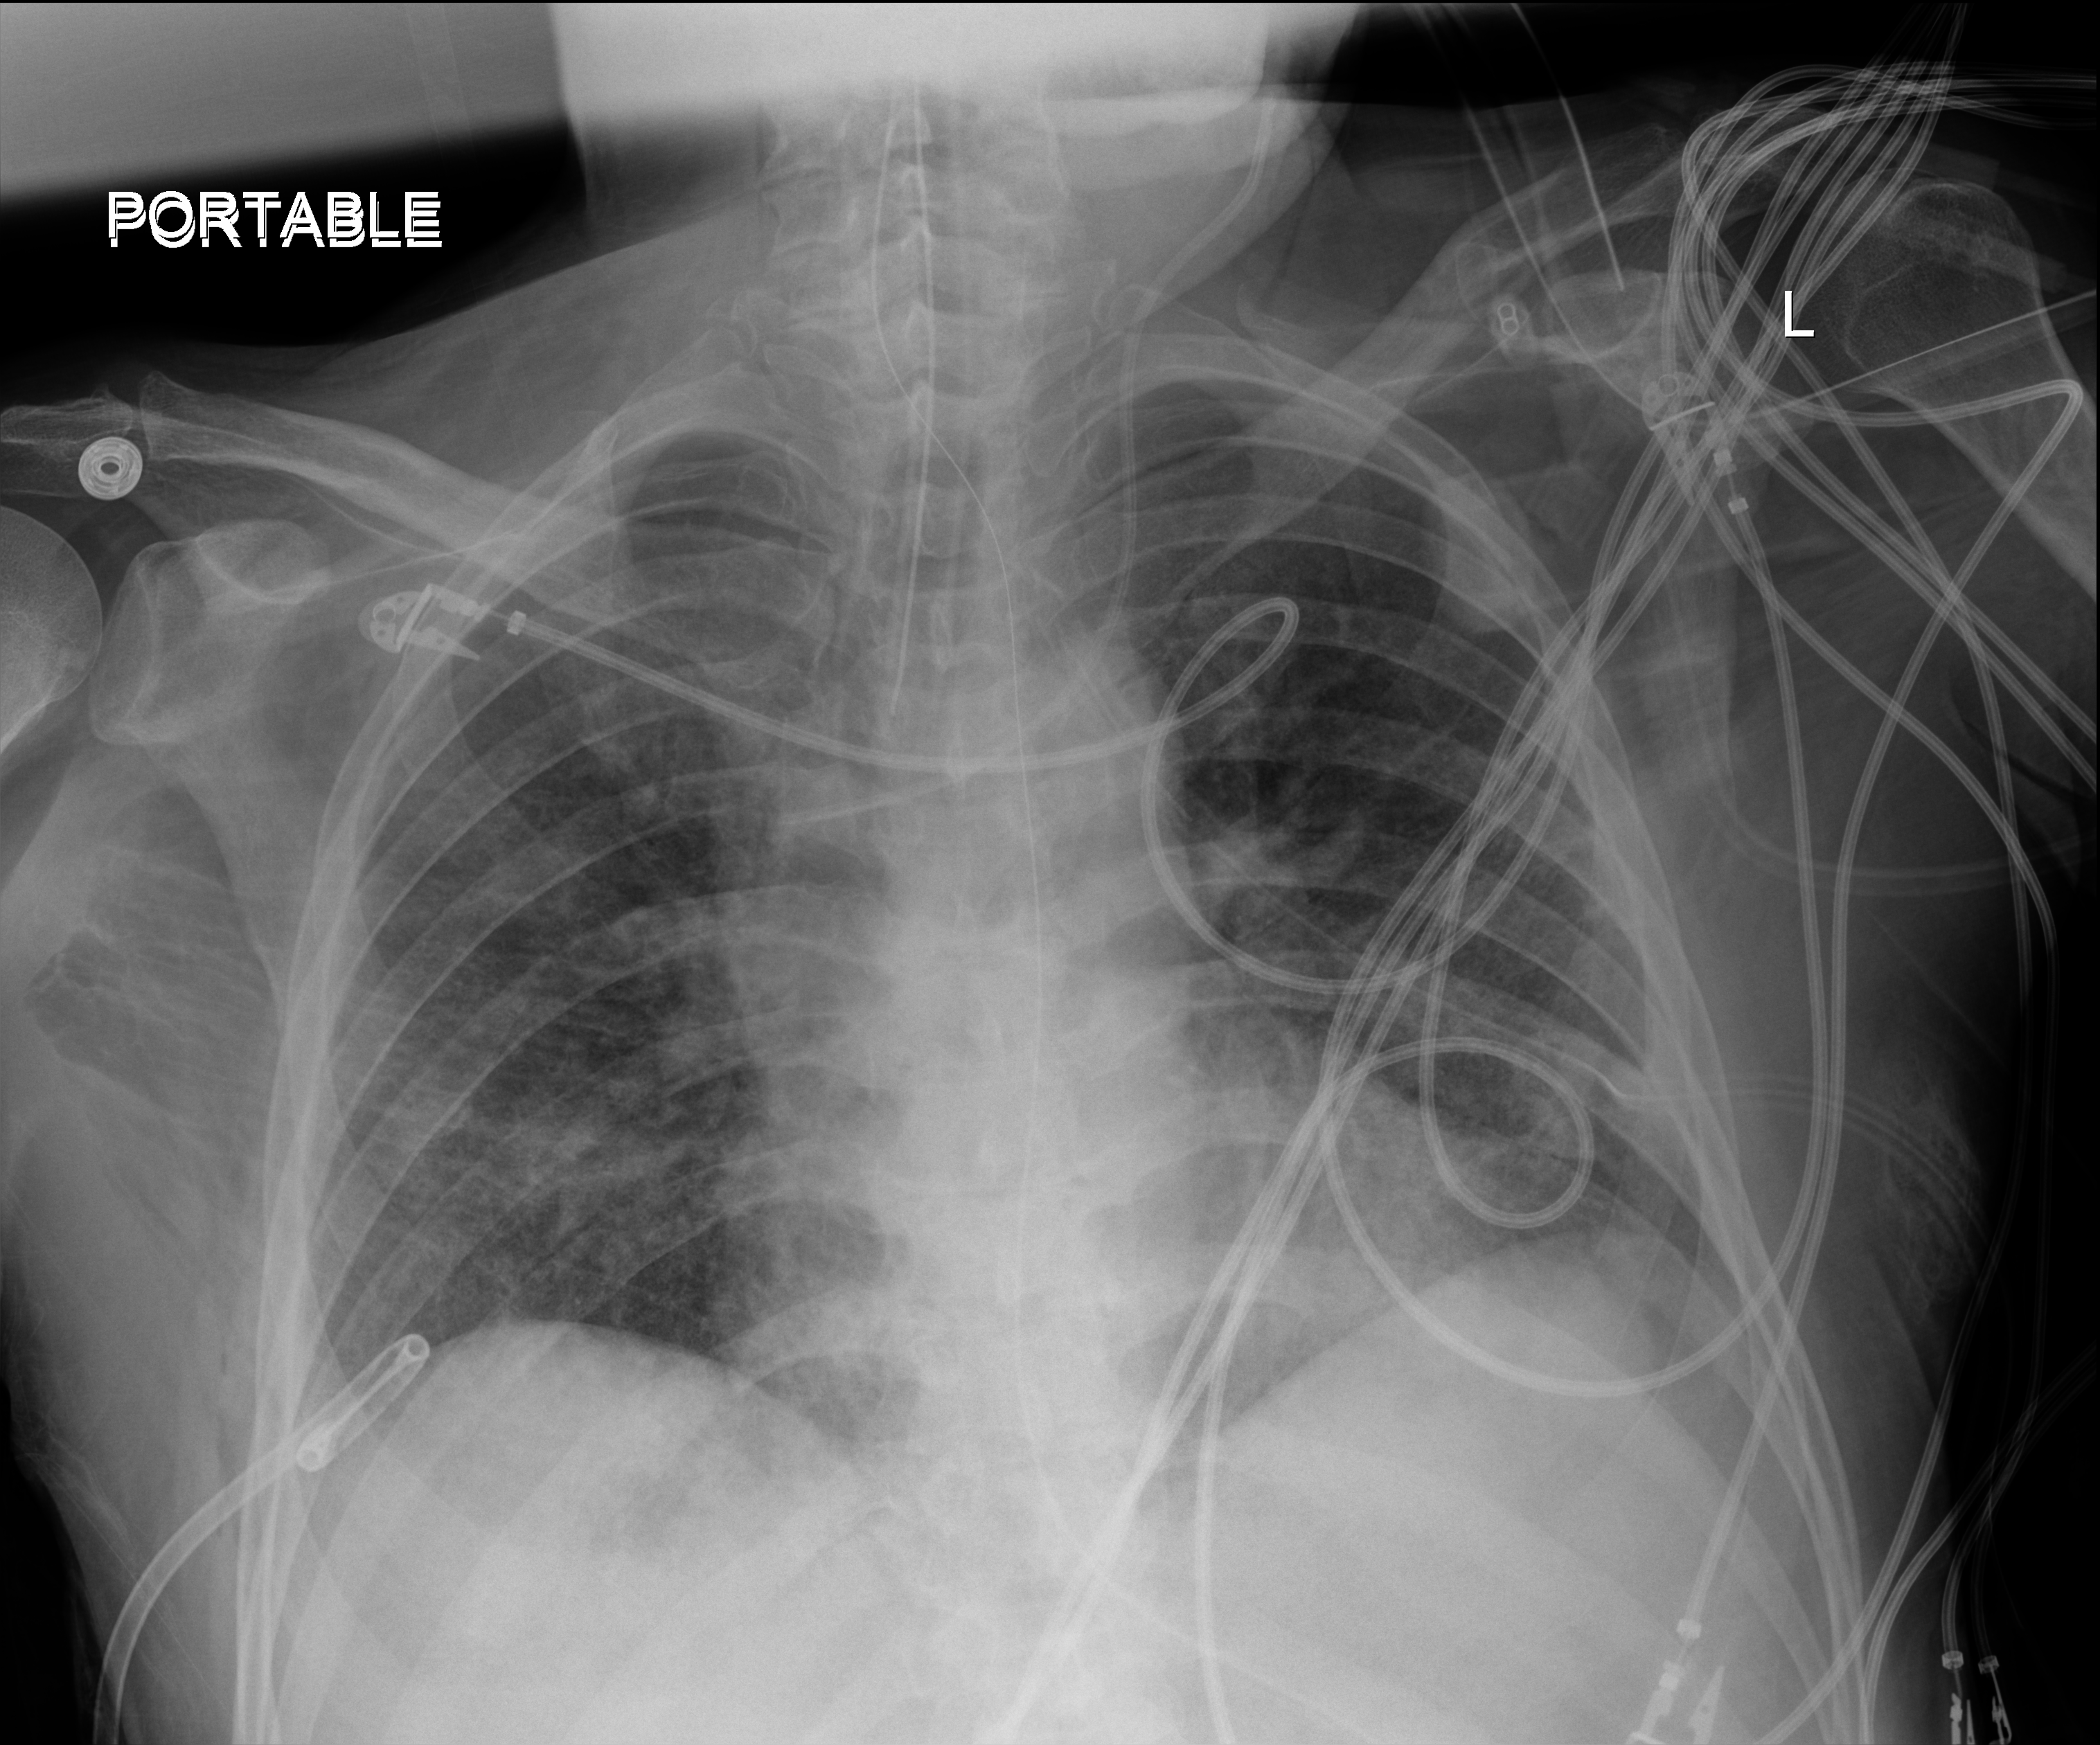
Chest radiograph (digital radiography); anteroposterior (AP) projection. Male patient hospitalised with COVID-19, age 18–59 years.
Admission-level facts for this patient (not findings on this image; timing relative to this image not recorded): mechanically ventilated during this hospital stay: yes; other chronic lung disease (admission record): no; length of hospital stay: 77 days.